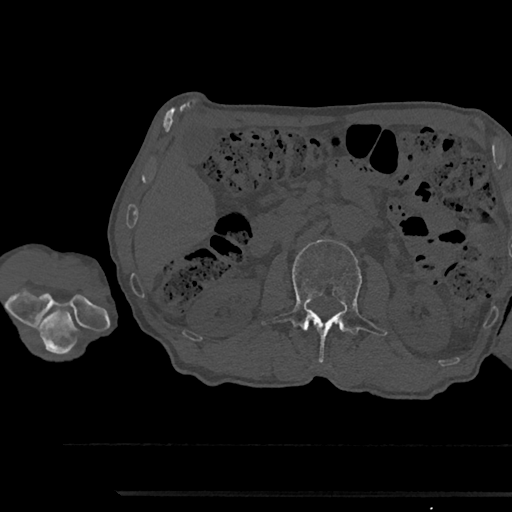
CT including the spine, one axial slice; reconstruction kernel Br40s/3; 120 kVp; bone window (W 1800 / L 400 HU); 0.5 mm slice thickness; 512 × 512 image matrix, field of view 367 × 367 mm. Patient: male, 79 years. From the clinical record (not read from this slice): primary cancer: prostate.
Outlined on this slice (semi-automatically segmented with operator editing):
- L2 vertebra: bounding box <261,240,387,364> (left, top, right, bottom; pixels)